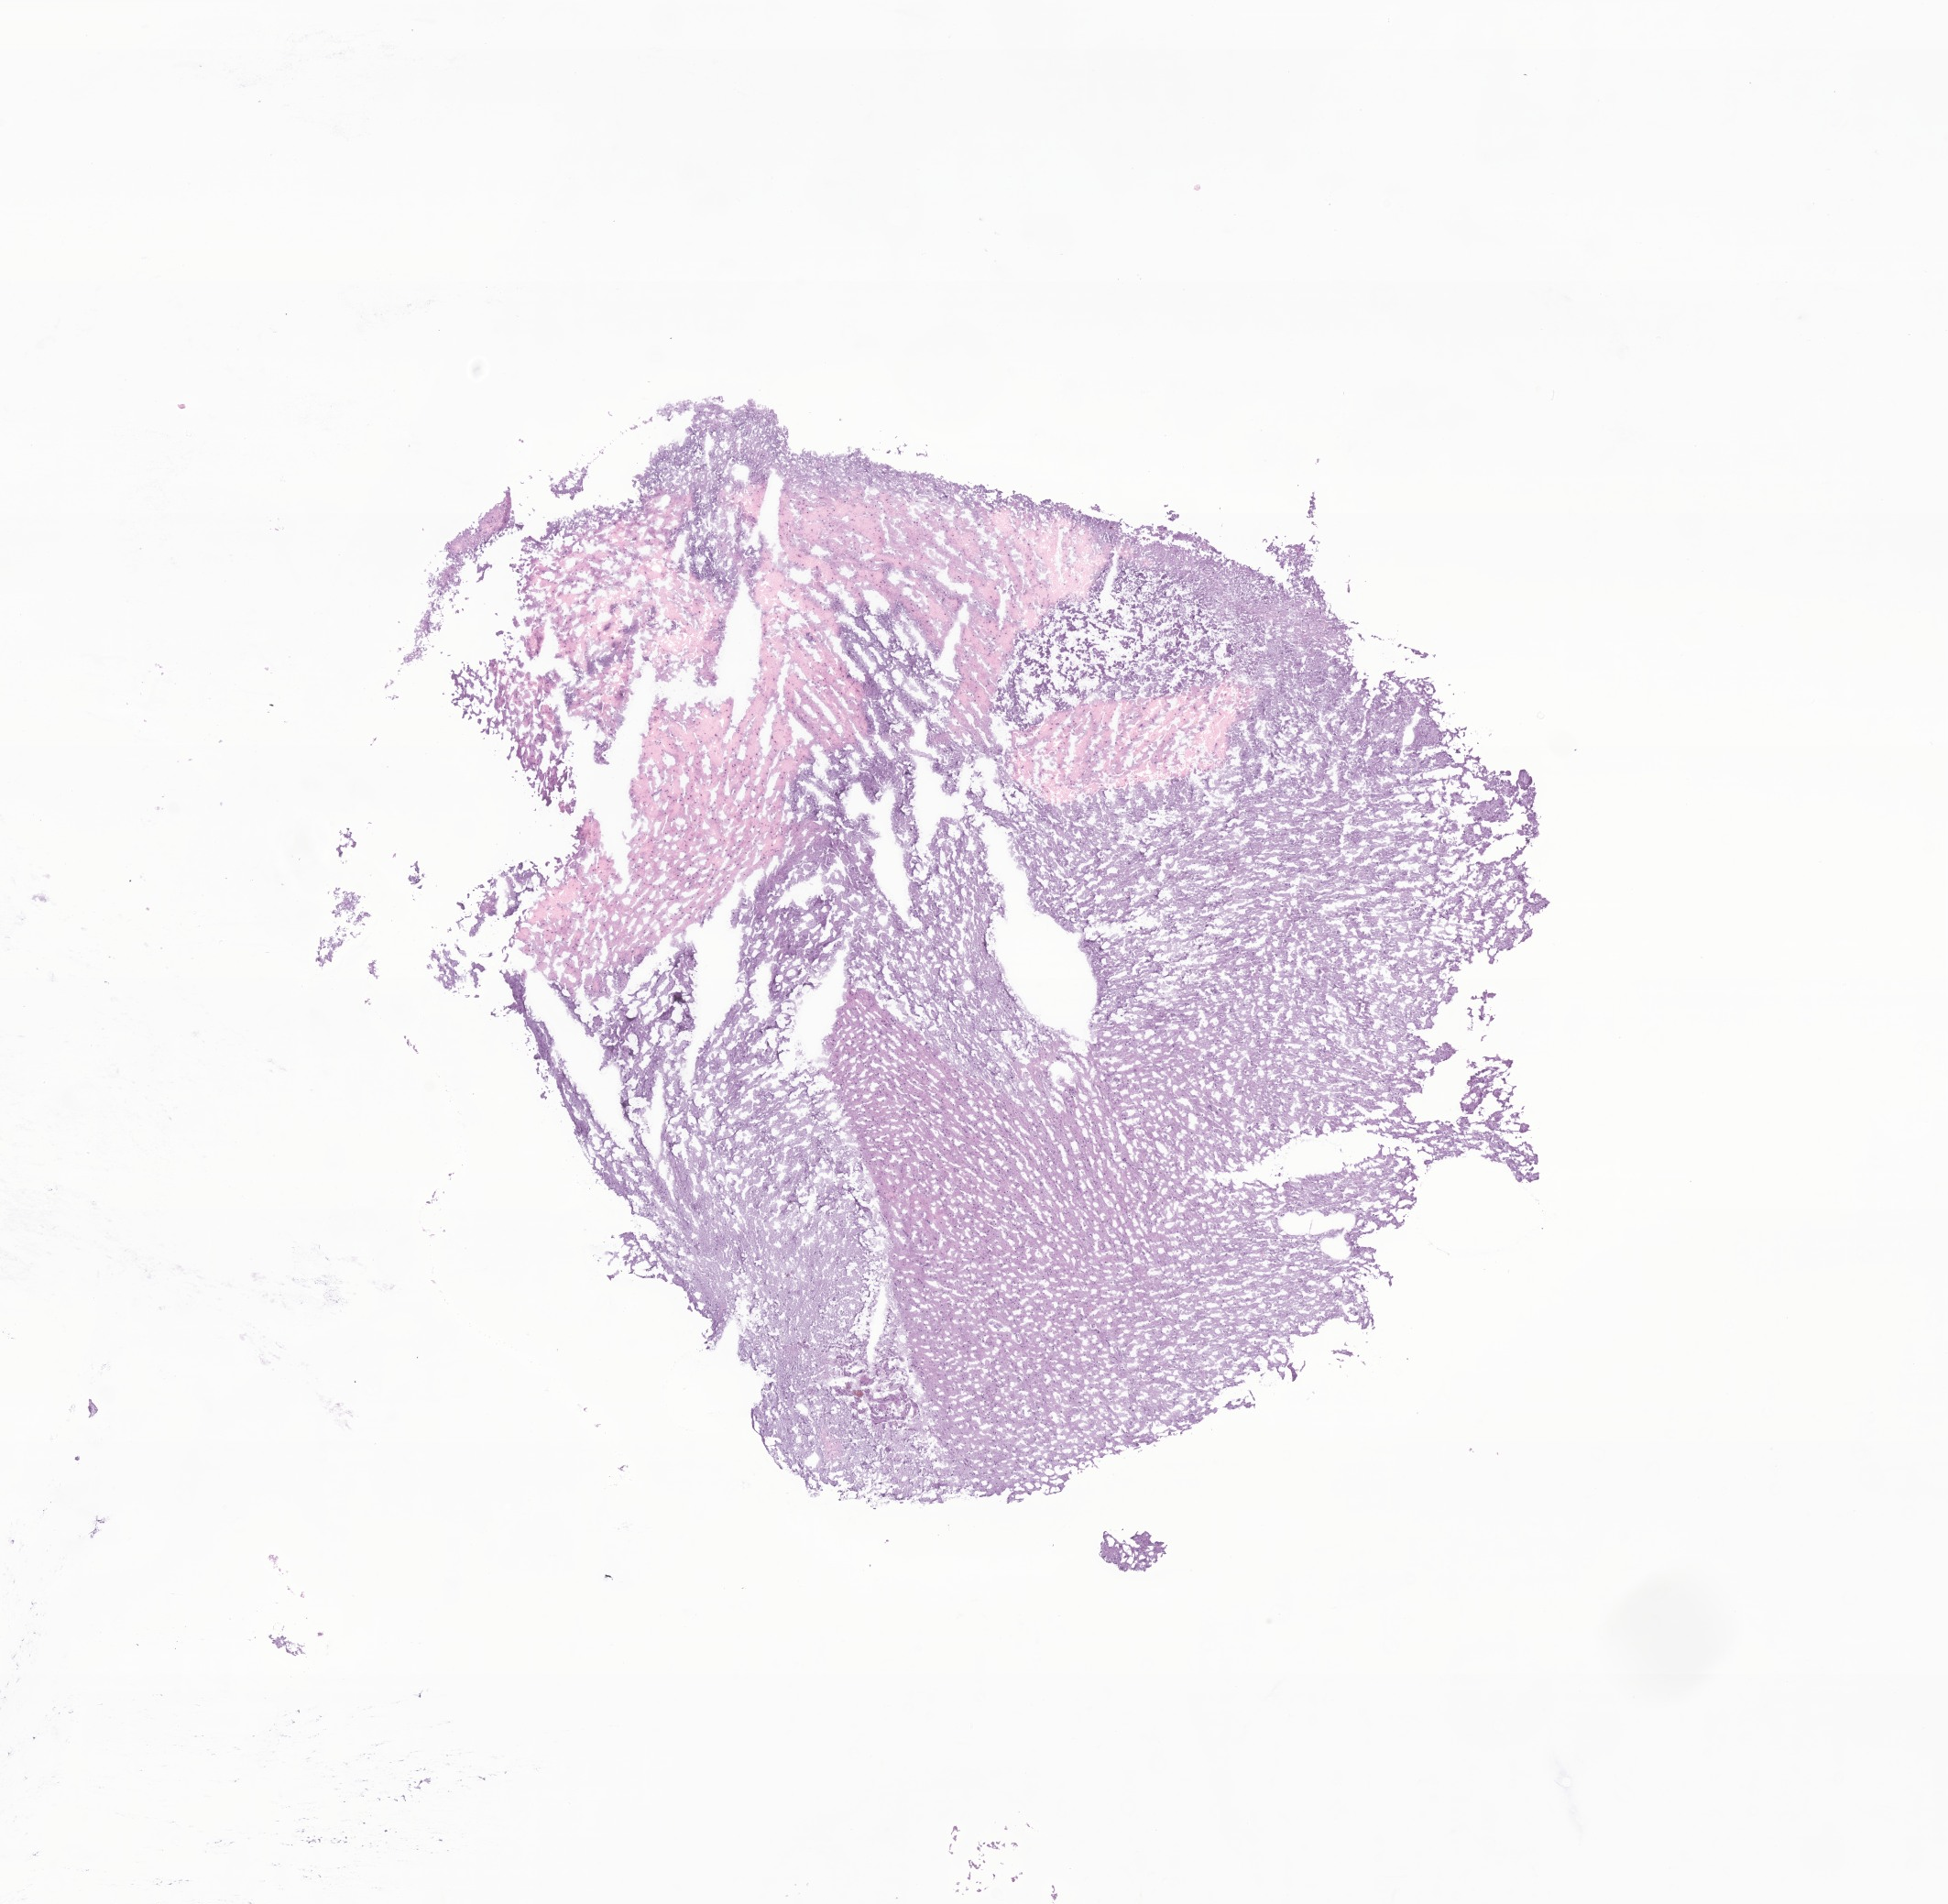
Digitized haematoxylin and eosin-stained section of tumor tissue from the brain — a low-resolution overview of the entire scanned area, about 9.0 x 8.8 mm. Cryosection (OCT / tissue freezing medium). Male patient, age 149 months (12 years 5 months).
* diagnosis: Glioma, malignant